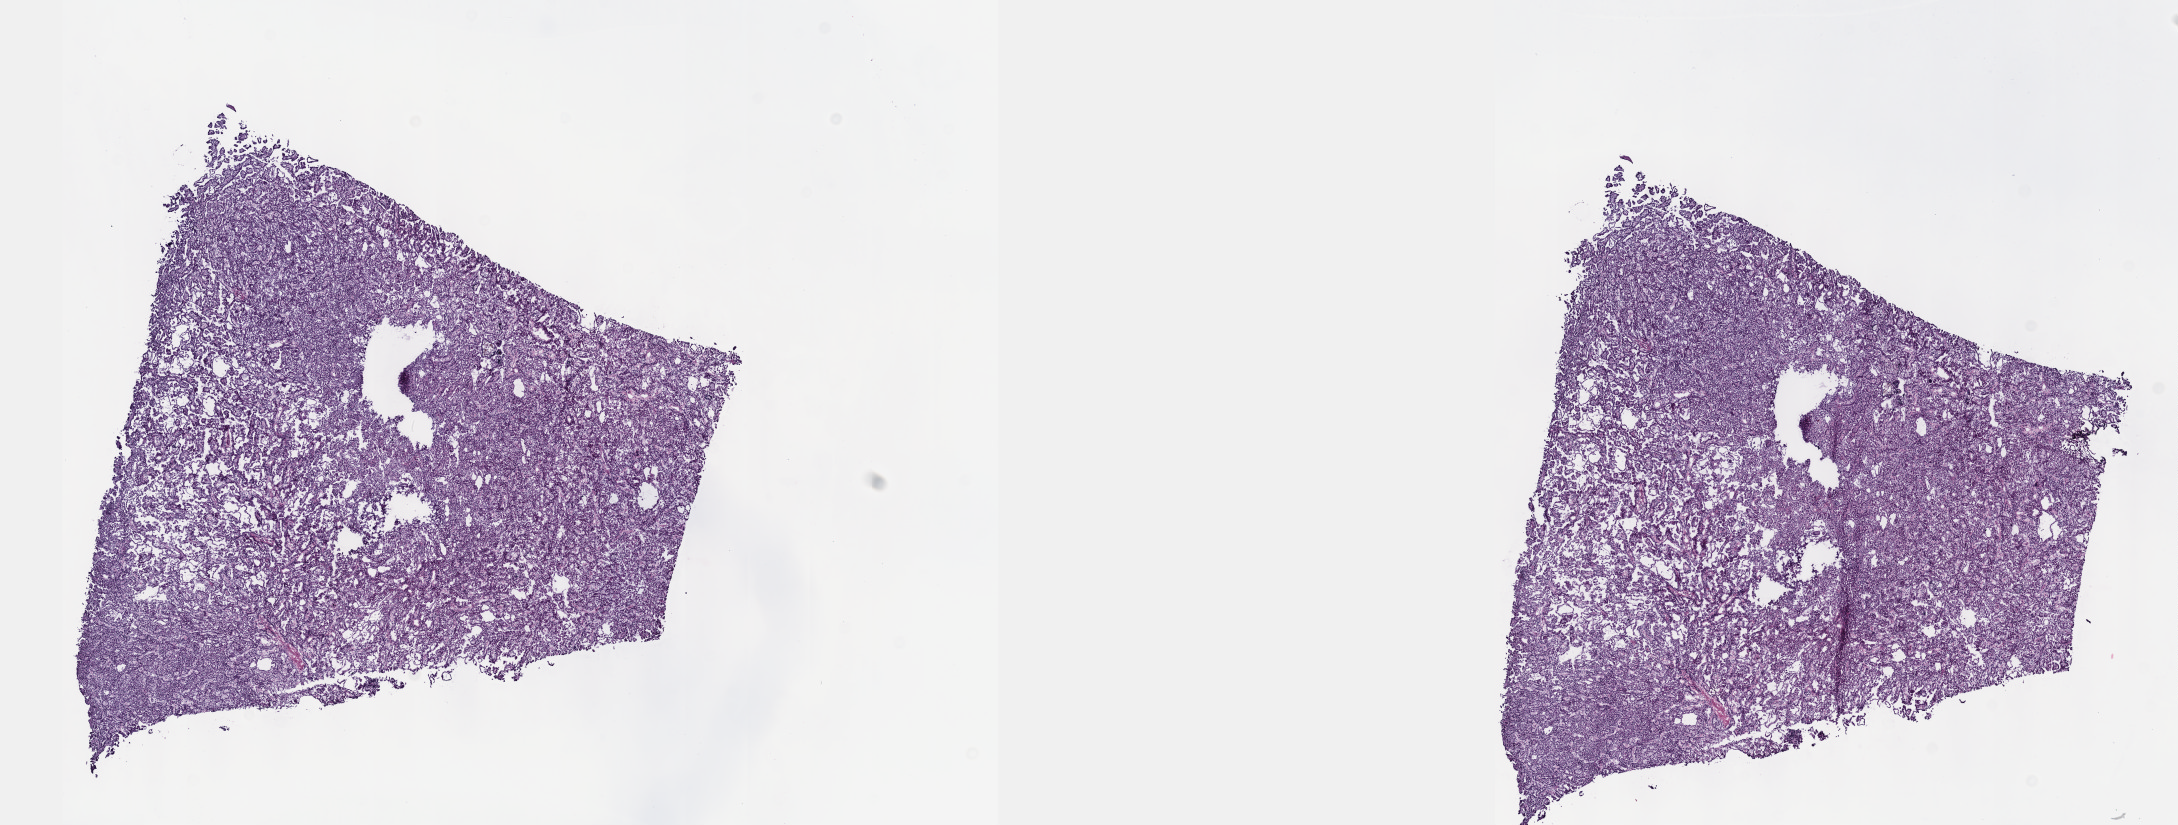
Digitized H&E tissue section (whole slide), low-resolution overview of the scanned area, about 17.6 x 6.7 mm (slide scanned at 40x); frozen section from the top of the tissue portion; sample: primary tumour, kidney. Male, age 47 years at initial diagnosis. Slide review estimates, as recorded: tumour cells 75%, tumour nuclei 75%, normal cells 0%, stromal cells 25%, necrosis 0%. Inflammatory infiltration, as recorded: lymphocyte infiltration 0%, monocyte infiltration 7%, neutrophil infiltration 0%.
AJCC pathologic stage: I. Diagnosis: Papillary adenocarcinoma, NOS.